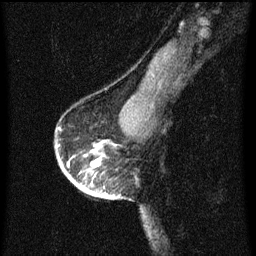
Breast MRI (dynamic contrast-enhanced), one sagittal slice. Dynamic contrast-enhanced series, image 2 of 3 at this slice position (ordered by acquisition). 1.5 T. TE 4.2 ms, TR 8 ms. 2 mm slice thickness. 256 × 256 image matrix, field of view 180 × 180 mm. Patient: female, 56 years.
Outlined on this slice (semi-automatic segmentation, software-assisted and operator-edited):
- analysis volume of interest (the breast-tissue region the enhancement analysis was run in; not a lesion): bounding box <55,126,120,199> (left, top, right, bottom; pixels)
- tumour enhancement mask (voxels above the 70 % enhancement threshold inside the analysis volume of interest): <56,128,113,197>